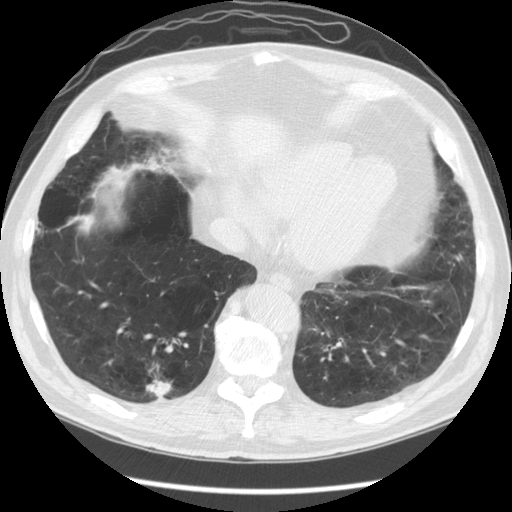
Low-dose screening chest CT, axial slice; baseline screening round; lung window (W 1500 / L -600 HU); 2.5 mm slice thickness; 512 × 512 image matrix. Male, age 67 years at enrolment. Former smoker at enrolment.
- Expert-annotated lung lesion, box from (x=121, y=356) to (x=185, y=414) px.
- The screening reader recorded 2 non-calcified nodules or masses ≥4 mm on this exam (right lower lobe, right lower lobe); which of them this box marks is not recorded.
- Official screen result: positive, change unspecified: nodule(s) >= 4 mm or enlarging nodule(s), mass(es), or other non-specific abnormalities suspicious for lung cancer.